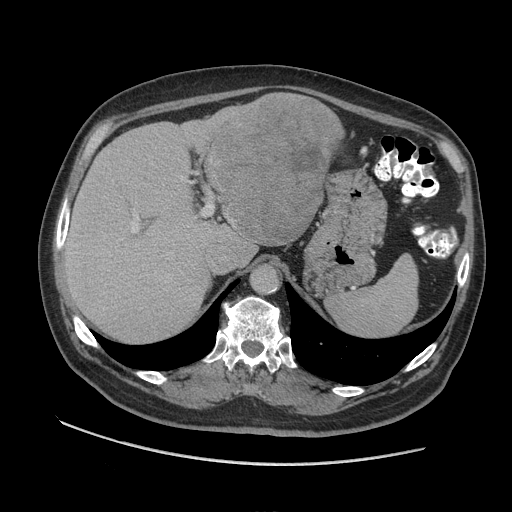
Contrast-enhanced abdominal CT (liver protocol), one axial slice. Slice 66 of 109 in the series (ordered by position). 140 kVp. Soft-tissue window (W 400 / L 40 HU). 512 × 512 image matrix, field of view 420 × 420 mm. Case-level facts recorded for this patient, not image findings: diagnosis: hepatocellular carcinoma (patient treated with transarterial chemoembolisation; whether this scan precedes or follows treatment is not stated here); TNM stage (as recorded): Stage-I; Child-Pugh class: A; tumour nodularity: uninodular.
Outlined on this slice (semi-automatic segmentation, software-assisted and operator-edited):
- liver parenchyma outside the tumour (the mass and vessels are separate outlines, so this box may not span the whole liver): box from (x=64, y=100) to (x=332, y=340) px
- mass: (x=176, y=92)–(x=345, y=245)
- liver vessels: (x=131, y=217)–(x=139, y=233)